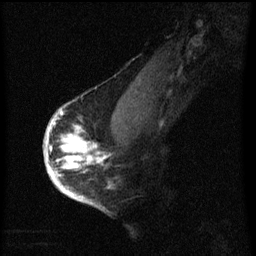
Breast MRI (dynamic contrast-enhanced), one sagittal slice; position 43 of 60 along the scan axis; dynamic contrast-enhanced series, image 2 of 3 at this slice position (ordered by acquisition); 1.5 T; TE 4.2 ms, TR 8 ms; 2 mm slice thickness; 256 × 256 image matrix, field of view 180 × 180 mm. Female patient, age 56 years.
Annotated regions visible in this slice (semi-automatically segmented with operator editing):
- analysis volume of interest (the breast-tissue region the enhancement analysis was run in; not a lesion): box from (x=46, y=110) to (x=107, y=193) px
- tumour enhancement mask (voxels above the 70 % enhancement threshold inside the analysis volume of interest): (x=46, y=110)–(x=107, y=193)